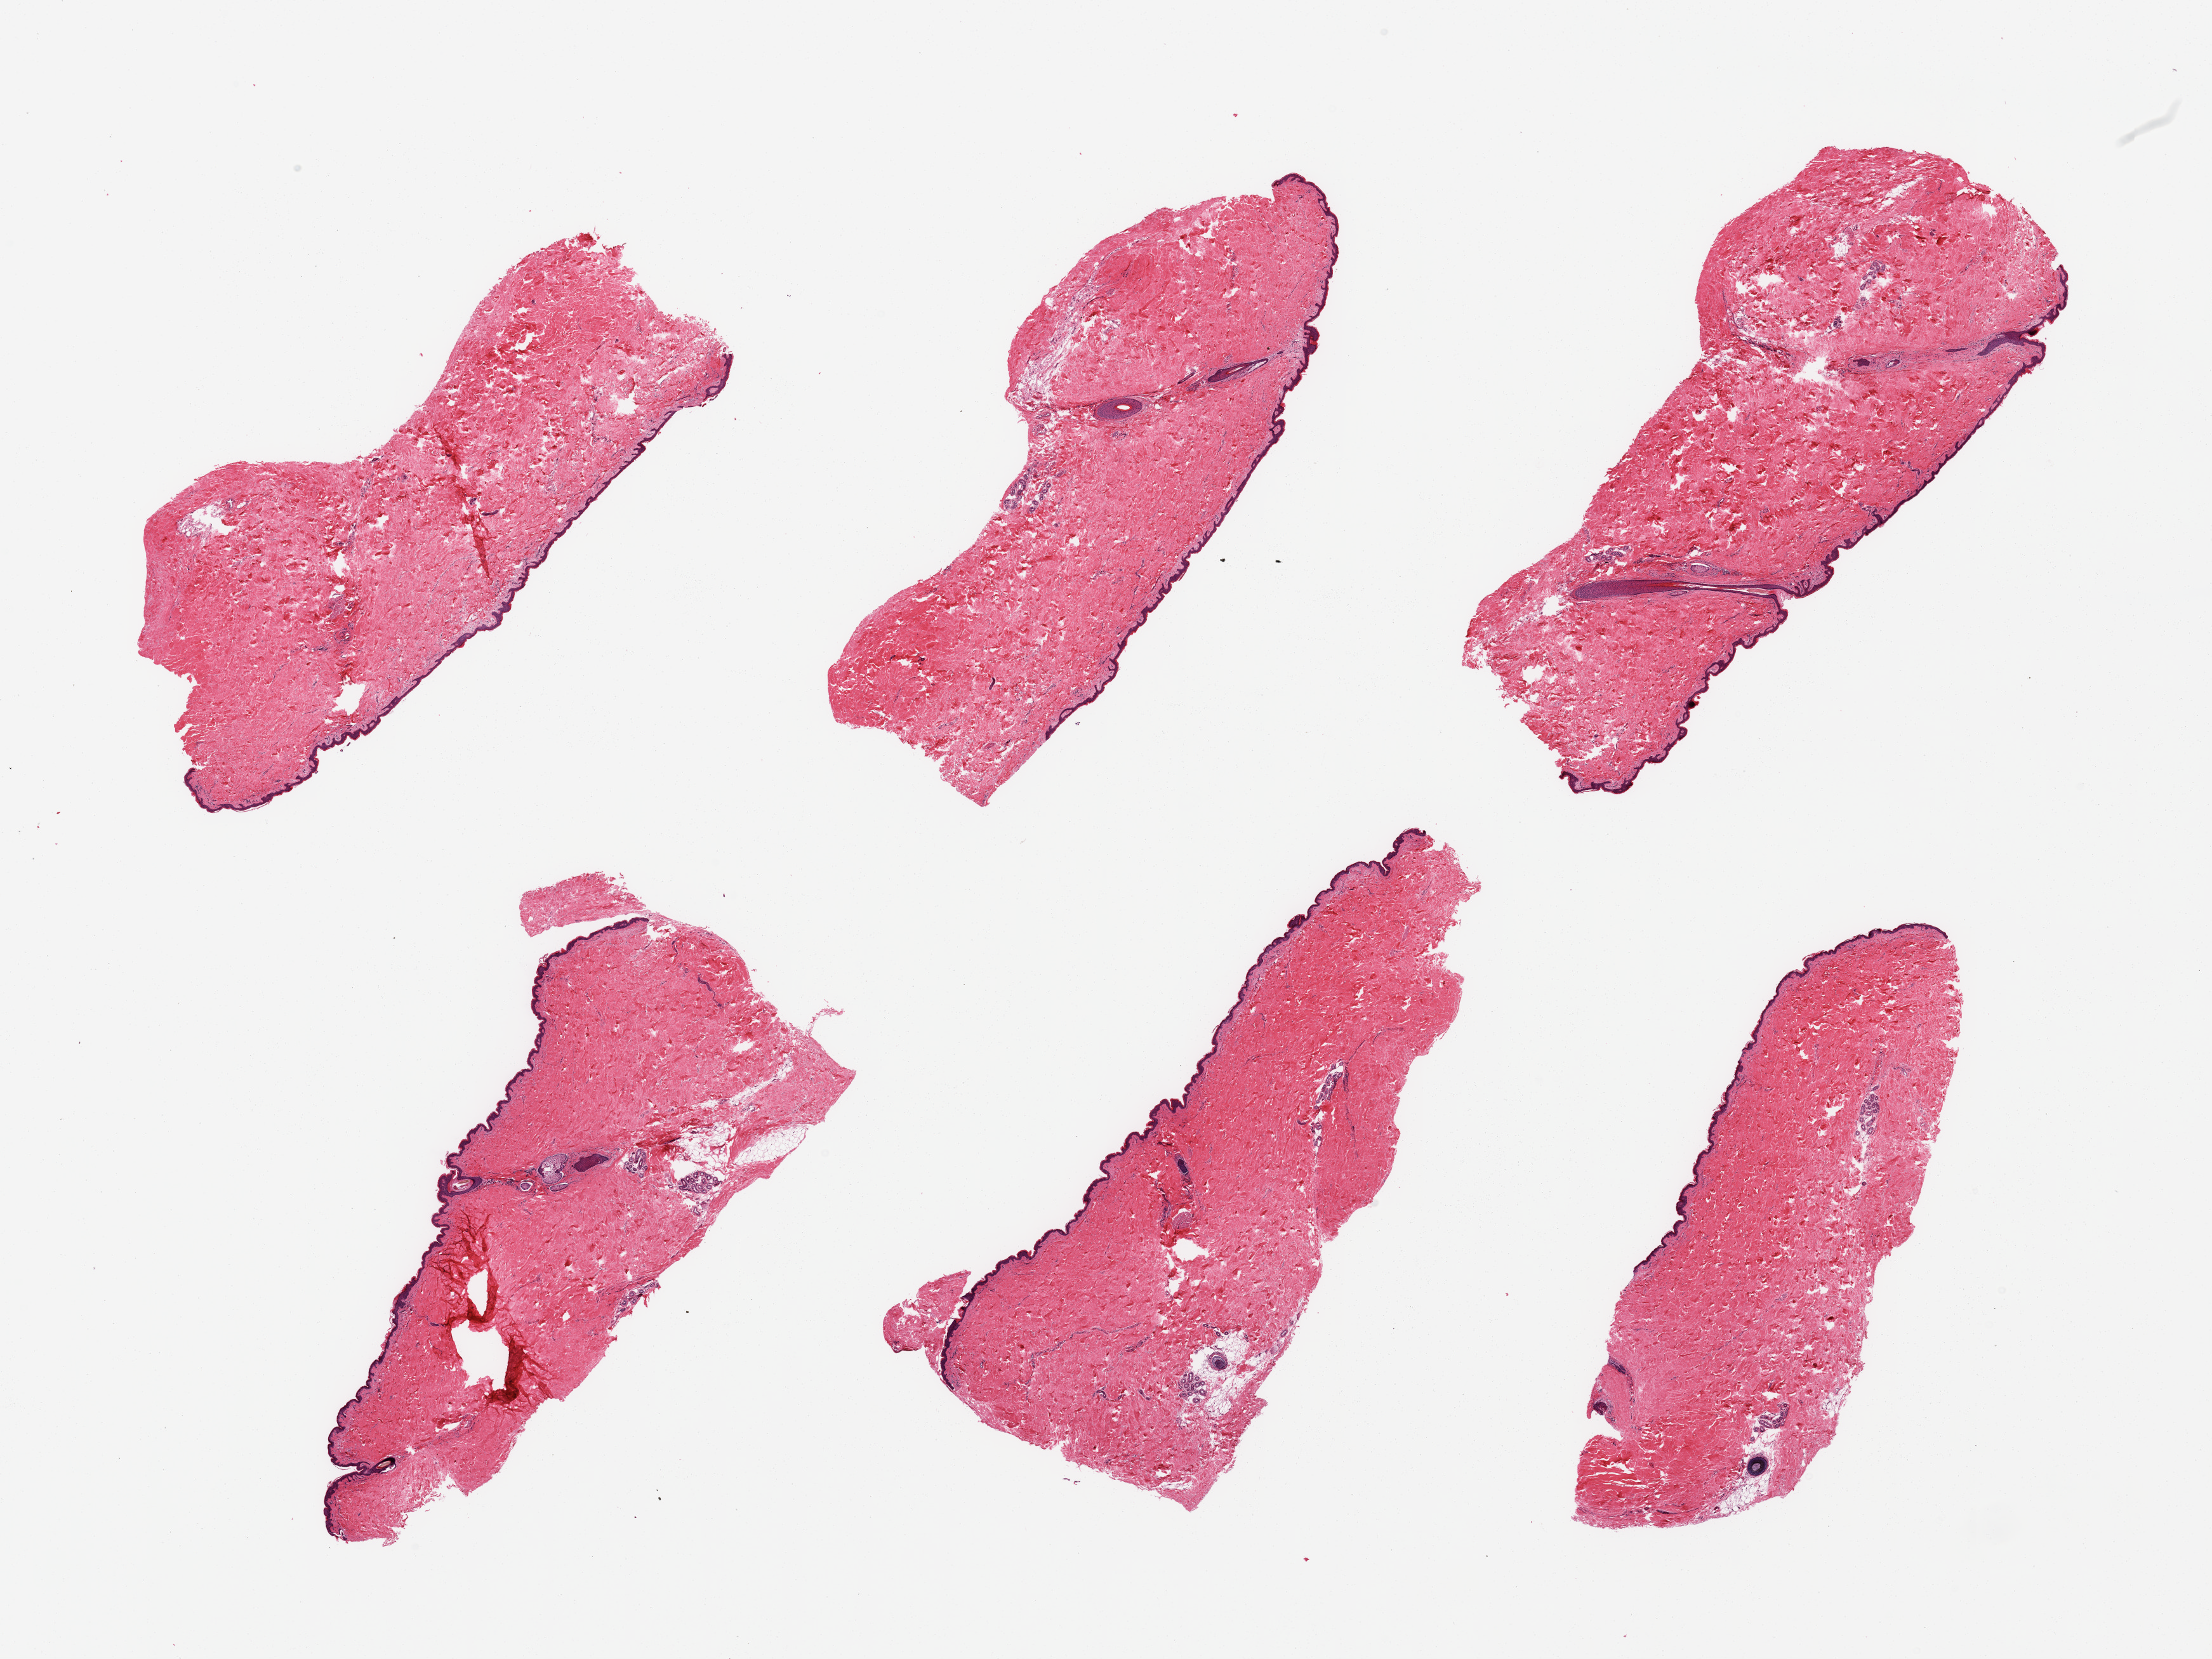
Digitized hematoxylin and eosin (H&E)-stained section, shown as a low-resolution overview of the whole scanned area (about 27.6 x 20.7 mm, slide scanned at 20x); PAXgene-fixed paraffin-embedded (PFPE) section; section of skin of suprapubic region (target tissue); tissue donor sample.
- reviewer comment on this tissue sample: 6 pieces; well trimmed; <5% dermal fat; several hair follicles